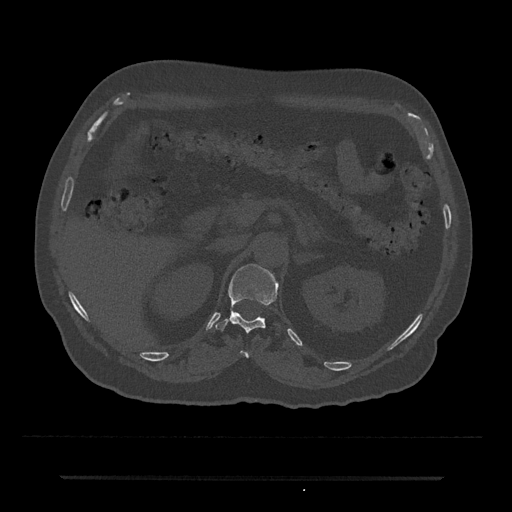
CT including the spine, one axial slice; position 126 of 797 along the scan axis; 120 kVp; bone window (W 1800 / L 400 HU); 0.5 mm slice thickness; 512 × 512 image matrix. Patient: male, 69 years. From the clinical record (not read from this slice): primary cancer: prostate.
Annotated regions visible in this slice (semi-automatic segmentation, software-assisted and operator-edited):
- T11 vertebra: bounding box (x1, y1, x2, y2) in pixels: (240, 351, 251, 358)
- T12 vertebra: (215, 264, 279, 335)